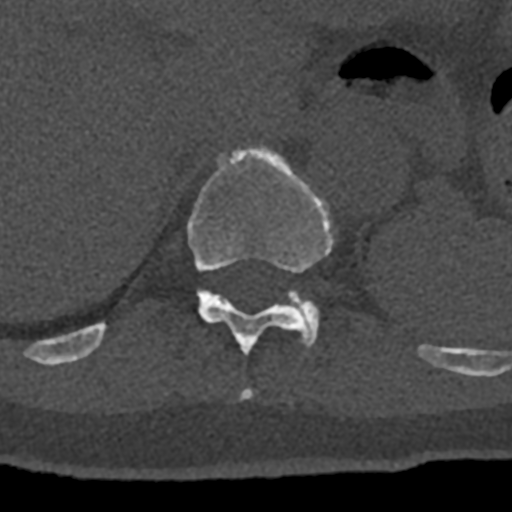
CT including the spine, one axial slice; slice 541 of 797 in the series (ordered by position); reconstruction kernel Br40s/3; 120 kVp; bone window (W 1800 / L 400 HU); 512 × 512 image matrix, field of view 160 × 160 mm. Patient: male, 74 years. Case-level facts recorded for this patient, not image findings: primary cancer: renal; vertebrae with lytic lesions (as recorded): T10, L1, L2, L3, L4, L5.
Outlined on this slice (semi-automatically segmented with operator editing):
- T10 vertebra: bounding box [x1, y1, x2, y2] px = [241, 388, 252, 399]
- T11 vertebra: [70, 144, 432, 363]
- T12 vertebra: [287, 290, 319, 342]